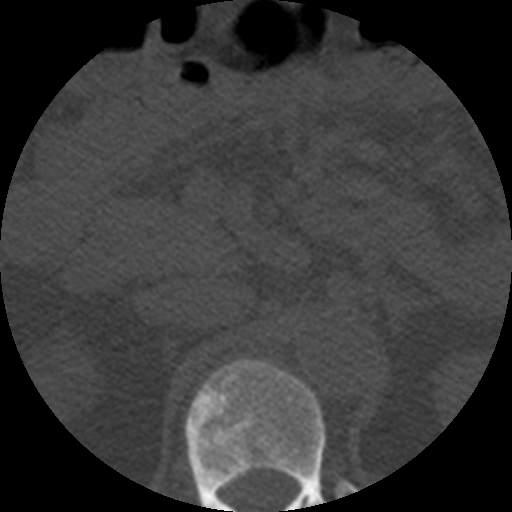
CT including the spine, one axial slice. Bone window (W 1800 / L 400 HU). 512 × 512 image matrix, field of view 160 × 160 mm. Patient age 57 years. From the clinical record (not read from this slice): primary cancer: prostate.
Annotated regions visible in this slice (semi-automatically segmented with operator editing):
- T12 vertebra: bounding box [x1, y1, x2, y2] px = [185, 358, 350, 512]